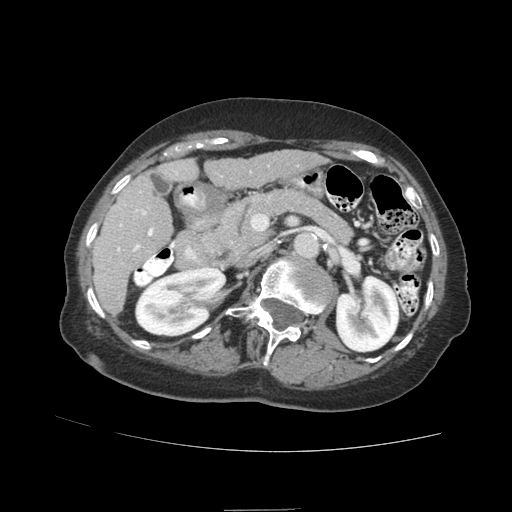
Contrast-enhanced abdominal CT (liver protocol), one axial slice. Position 38 of 89 along the scan axis. Reconstruction kernel STANDARD. Soft-tissue window (W 400 / L 40 HU). 2.5 mm slice thickness. 512 × 512 image matrix, field of view 360 × 360 mm. Case-level facts recorded for this patient, not image findings: diagnosis: hepatocellular carcinoma (patient treated with transarterial chemoembolisation; whether this scan precedes or follows treatment is not stated here); TNM stage (as recorded): Stage-II; Child-Pugh class: A; tumour differentiation: moderately differentiated; tumour nodularity: multinodular.
Annotated regions visible in this slice (semi-automatic segmentation, software-assisted and operator-edited):
- liver parenchyma outside the tumour (the mass and vessels are separate outlines, so this box may not span the whole liver): bounding box (x1, y1, x2, y2) in pixels: (92, 150, 322, 314)
- liver vessels: (117, 171, 222, 252)